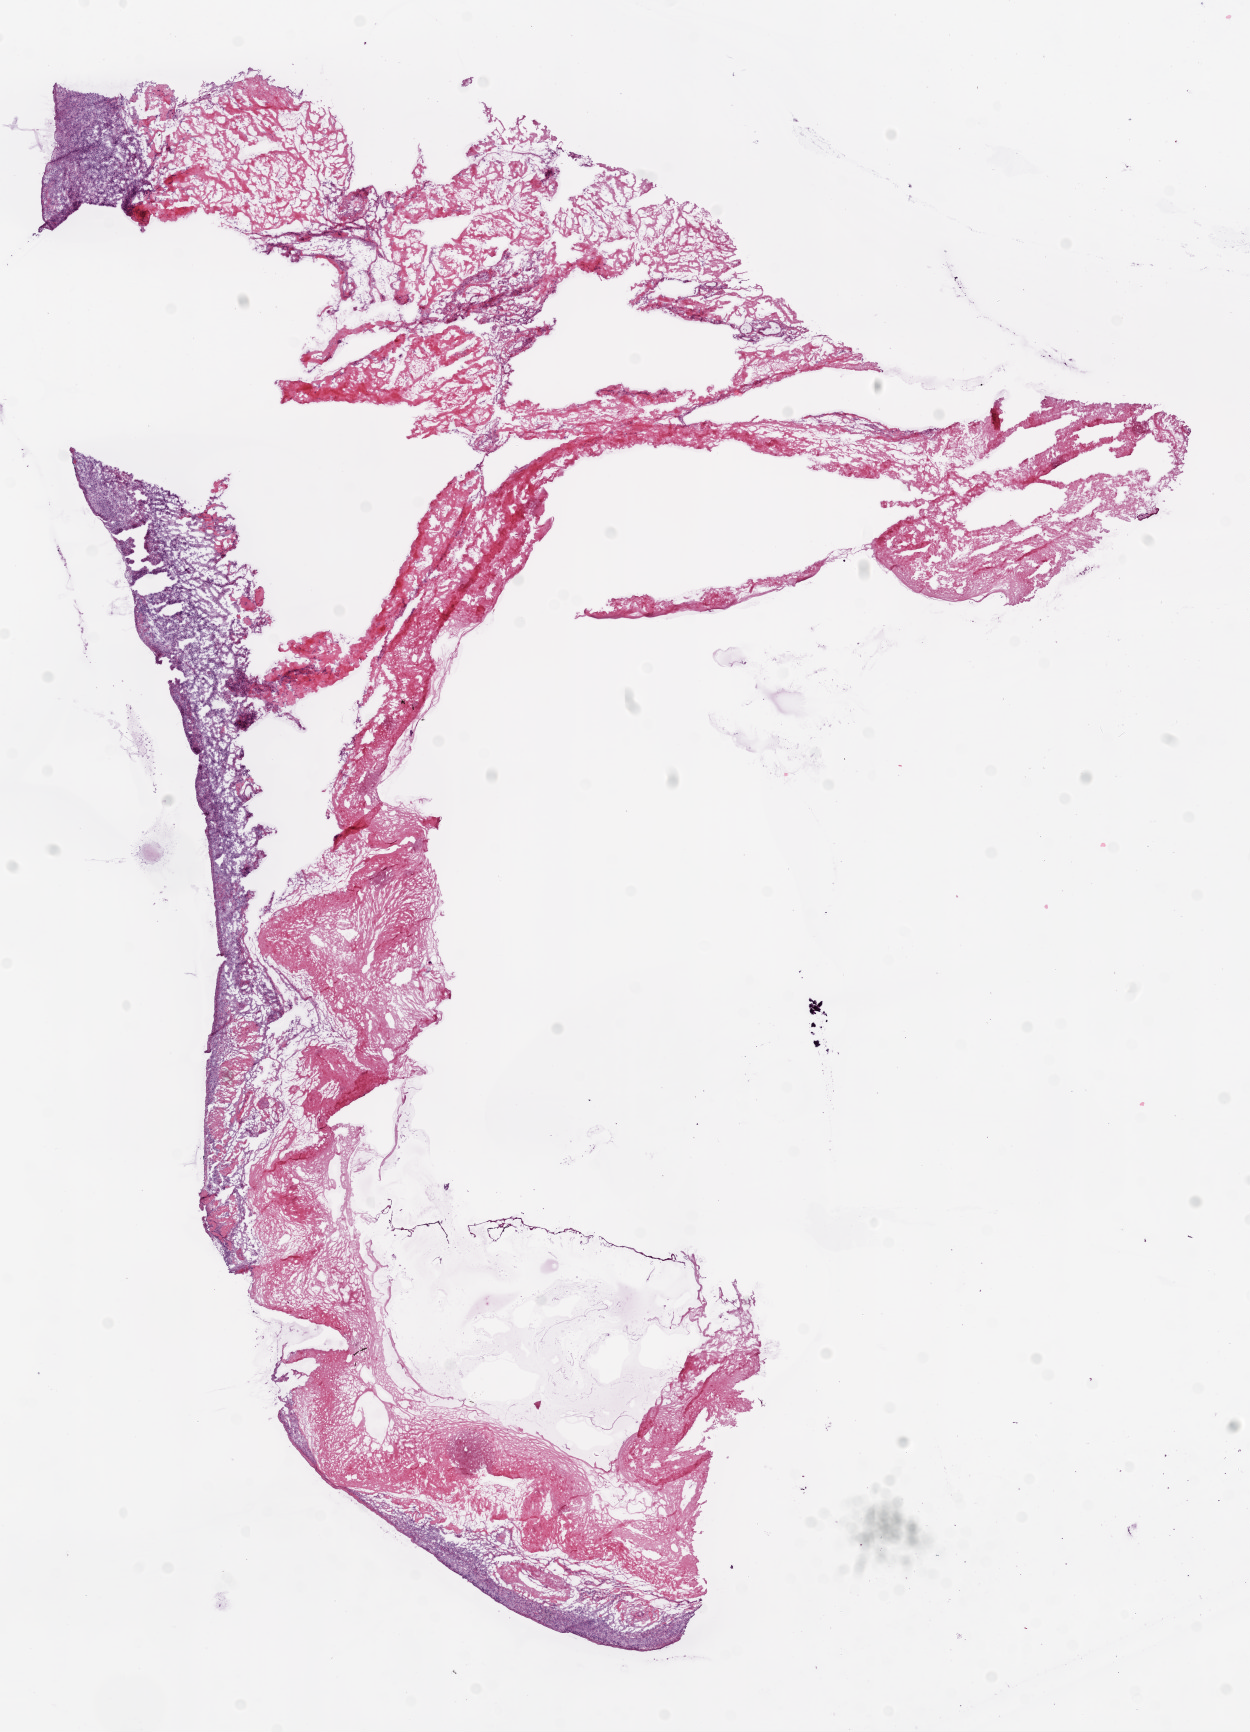
Whole-slide histology image, H&E — low-resolution overview of the scanned area, about 10.0 x 13.9 mm, frozen section from the bottom of the tissue portion, solid tissue normal (non-tumour tissue) sample from the ovary. Female, age 74 years at initial diagnosis.
This section: solid tissue normal (non-tumour) sample from the same patient. Patient diagnosis: Serous cystadenocarcinoma, NOS.